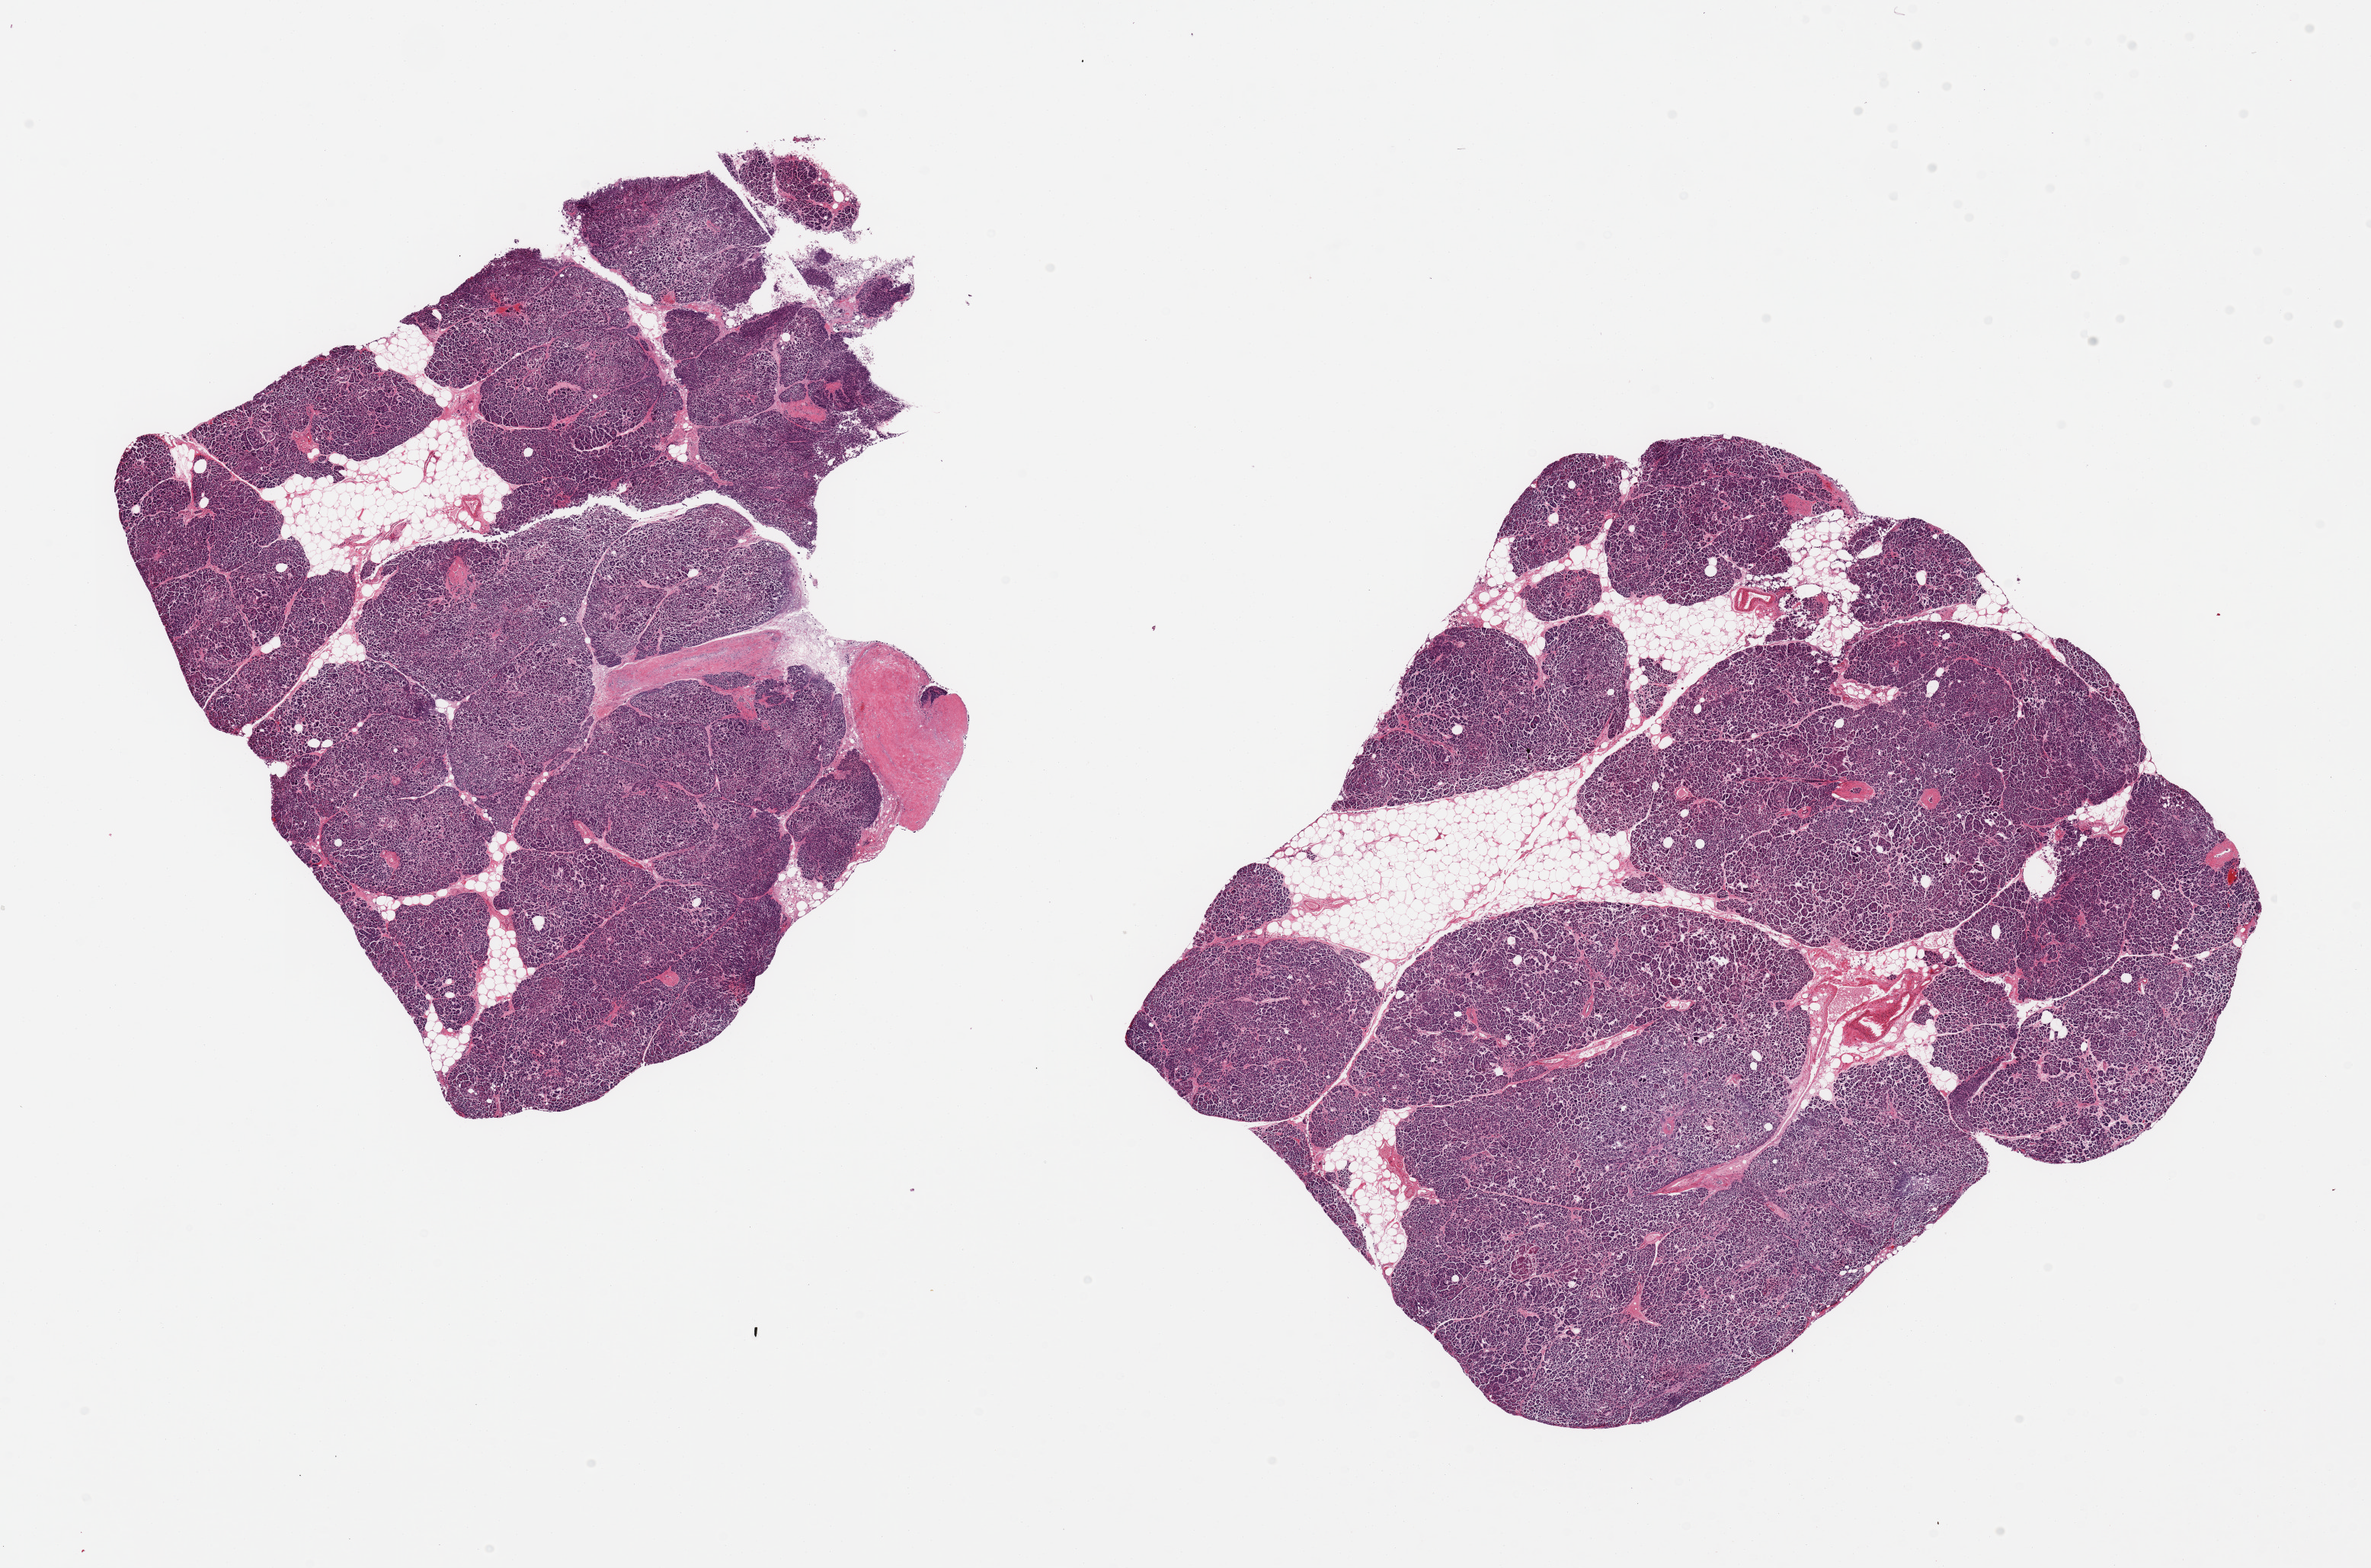
H&E whole-slide image, whole scanned area (about 24.6 x 16.3 mm) shown as a low-resolution overview; PAXgene-fixed, paraffin-embedded tissue; sampled site (target tissue): pancreas; donor tissue sample. Male donor.
* reviewer comment on this tissue sample: 2 pieces; 20% internal fat content